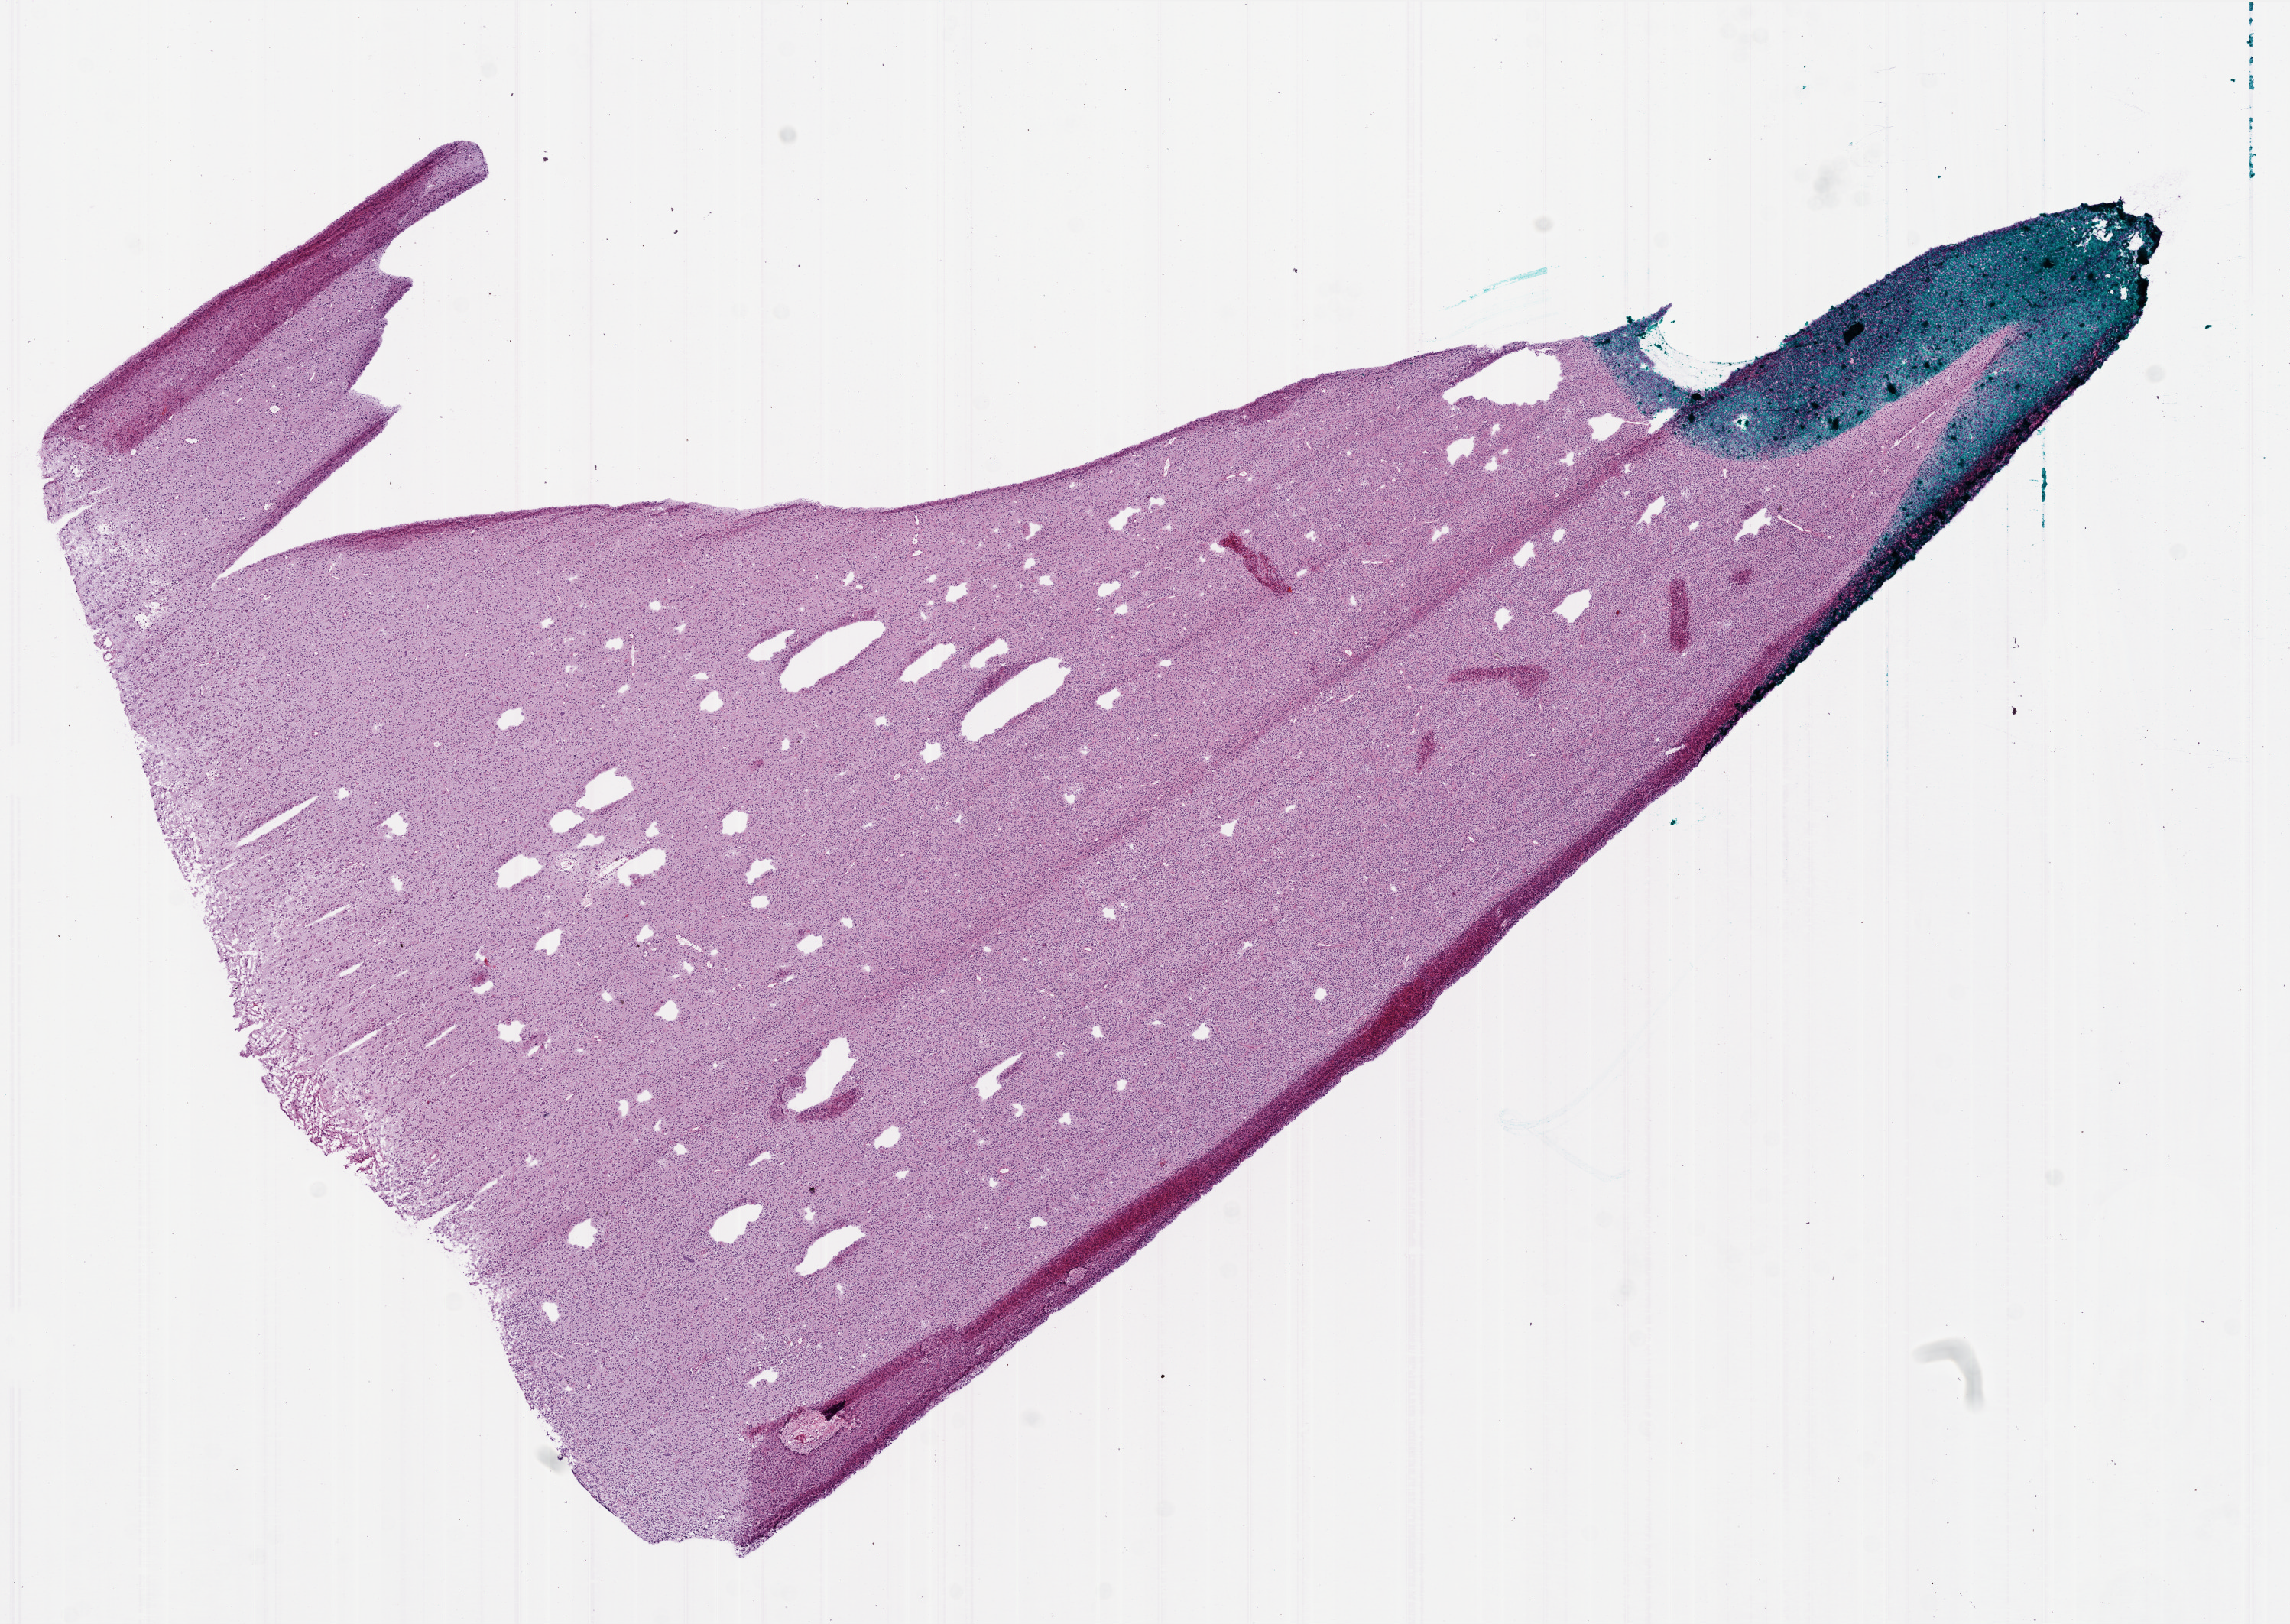
Digitized Hematoxylin and eosin (H&E) stained tissue section (whole slide) — shown as a low-resolution overview of the whole scanned area (about 12.0 x 8.5 mm, slide scanned at 20x); frozen section from the bottom of the tissue portion; sample: primary tumour, brain. Male, age 59 years at initial diagnosis. Slide review estimates, as recorded: tumour cells 95%, tumour nuclei 95%.
Histologic diagnosis: Glioblastoma.